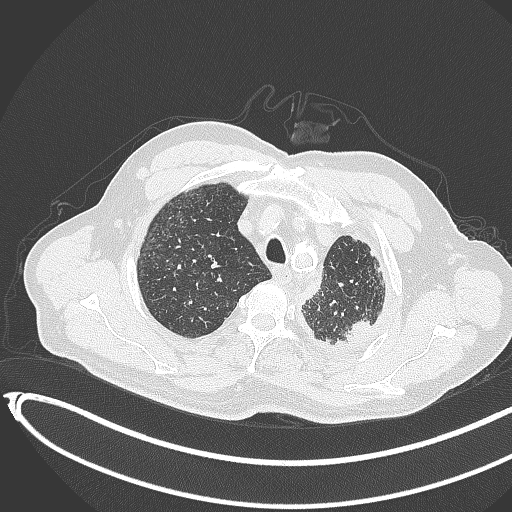
Chest CT, one axial slice. Slice 360 of 451 in the series (ordered by position). Reconstruction kernel B70f. Lung window (W 1500 / L -600 HU). 1 mm slice thickness. 512 × 512 image matrix, field of view 400 × 400 mm. Patient: male, 78 years. Case-level facts recorded for this patient, not image findings: clinical TNM (as recorded): T1c N0 M1.
Annotated regions visible in this slice (rectangle marked by the reading radiologist):
- lung tumour (recorded histology: adenocarcinoma): bounding box (x1, y1, x2, y2) in pixels: (341, 311, 376, 348)